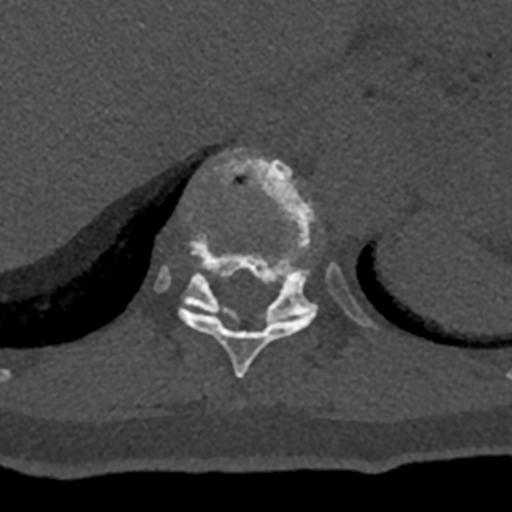
CT including the spine, one axial slice; slice 582 of 797 in the series (ordered by position); reconstruction kernel Br40s/3; 120 kVp; bone window (W 1800 / L 400 HU); 512 × 512 image matrix, field of view 160 × 160 mm. Patient: male, 74 years. Case-level facts recorded for this patient, not image findings: primary cancer: renal; vertebrae with lytic lesions (as recorded): T10, L1, L2, L3, L4, L5.
Structures marked on this image (semi-automatic segmentation, software-assisted and operator-edited):
- T10 vertebra: box from (x=178, y=149) to (x=316, y=378) px
- T11 vertebra: (x=155, y=150)–(x=374, y=327)